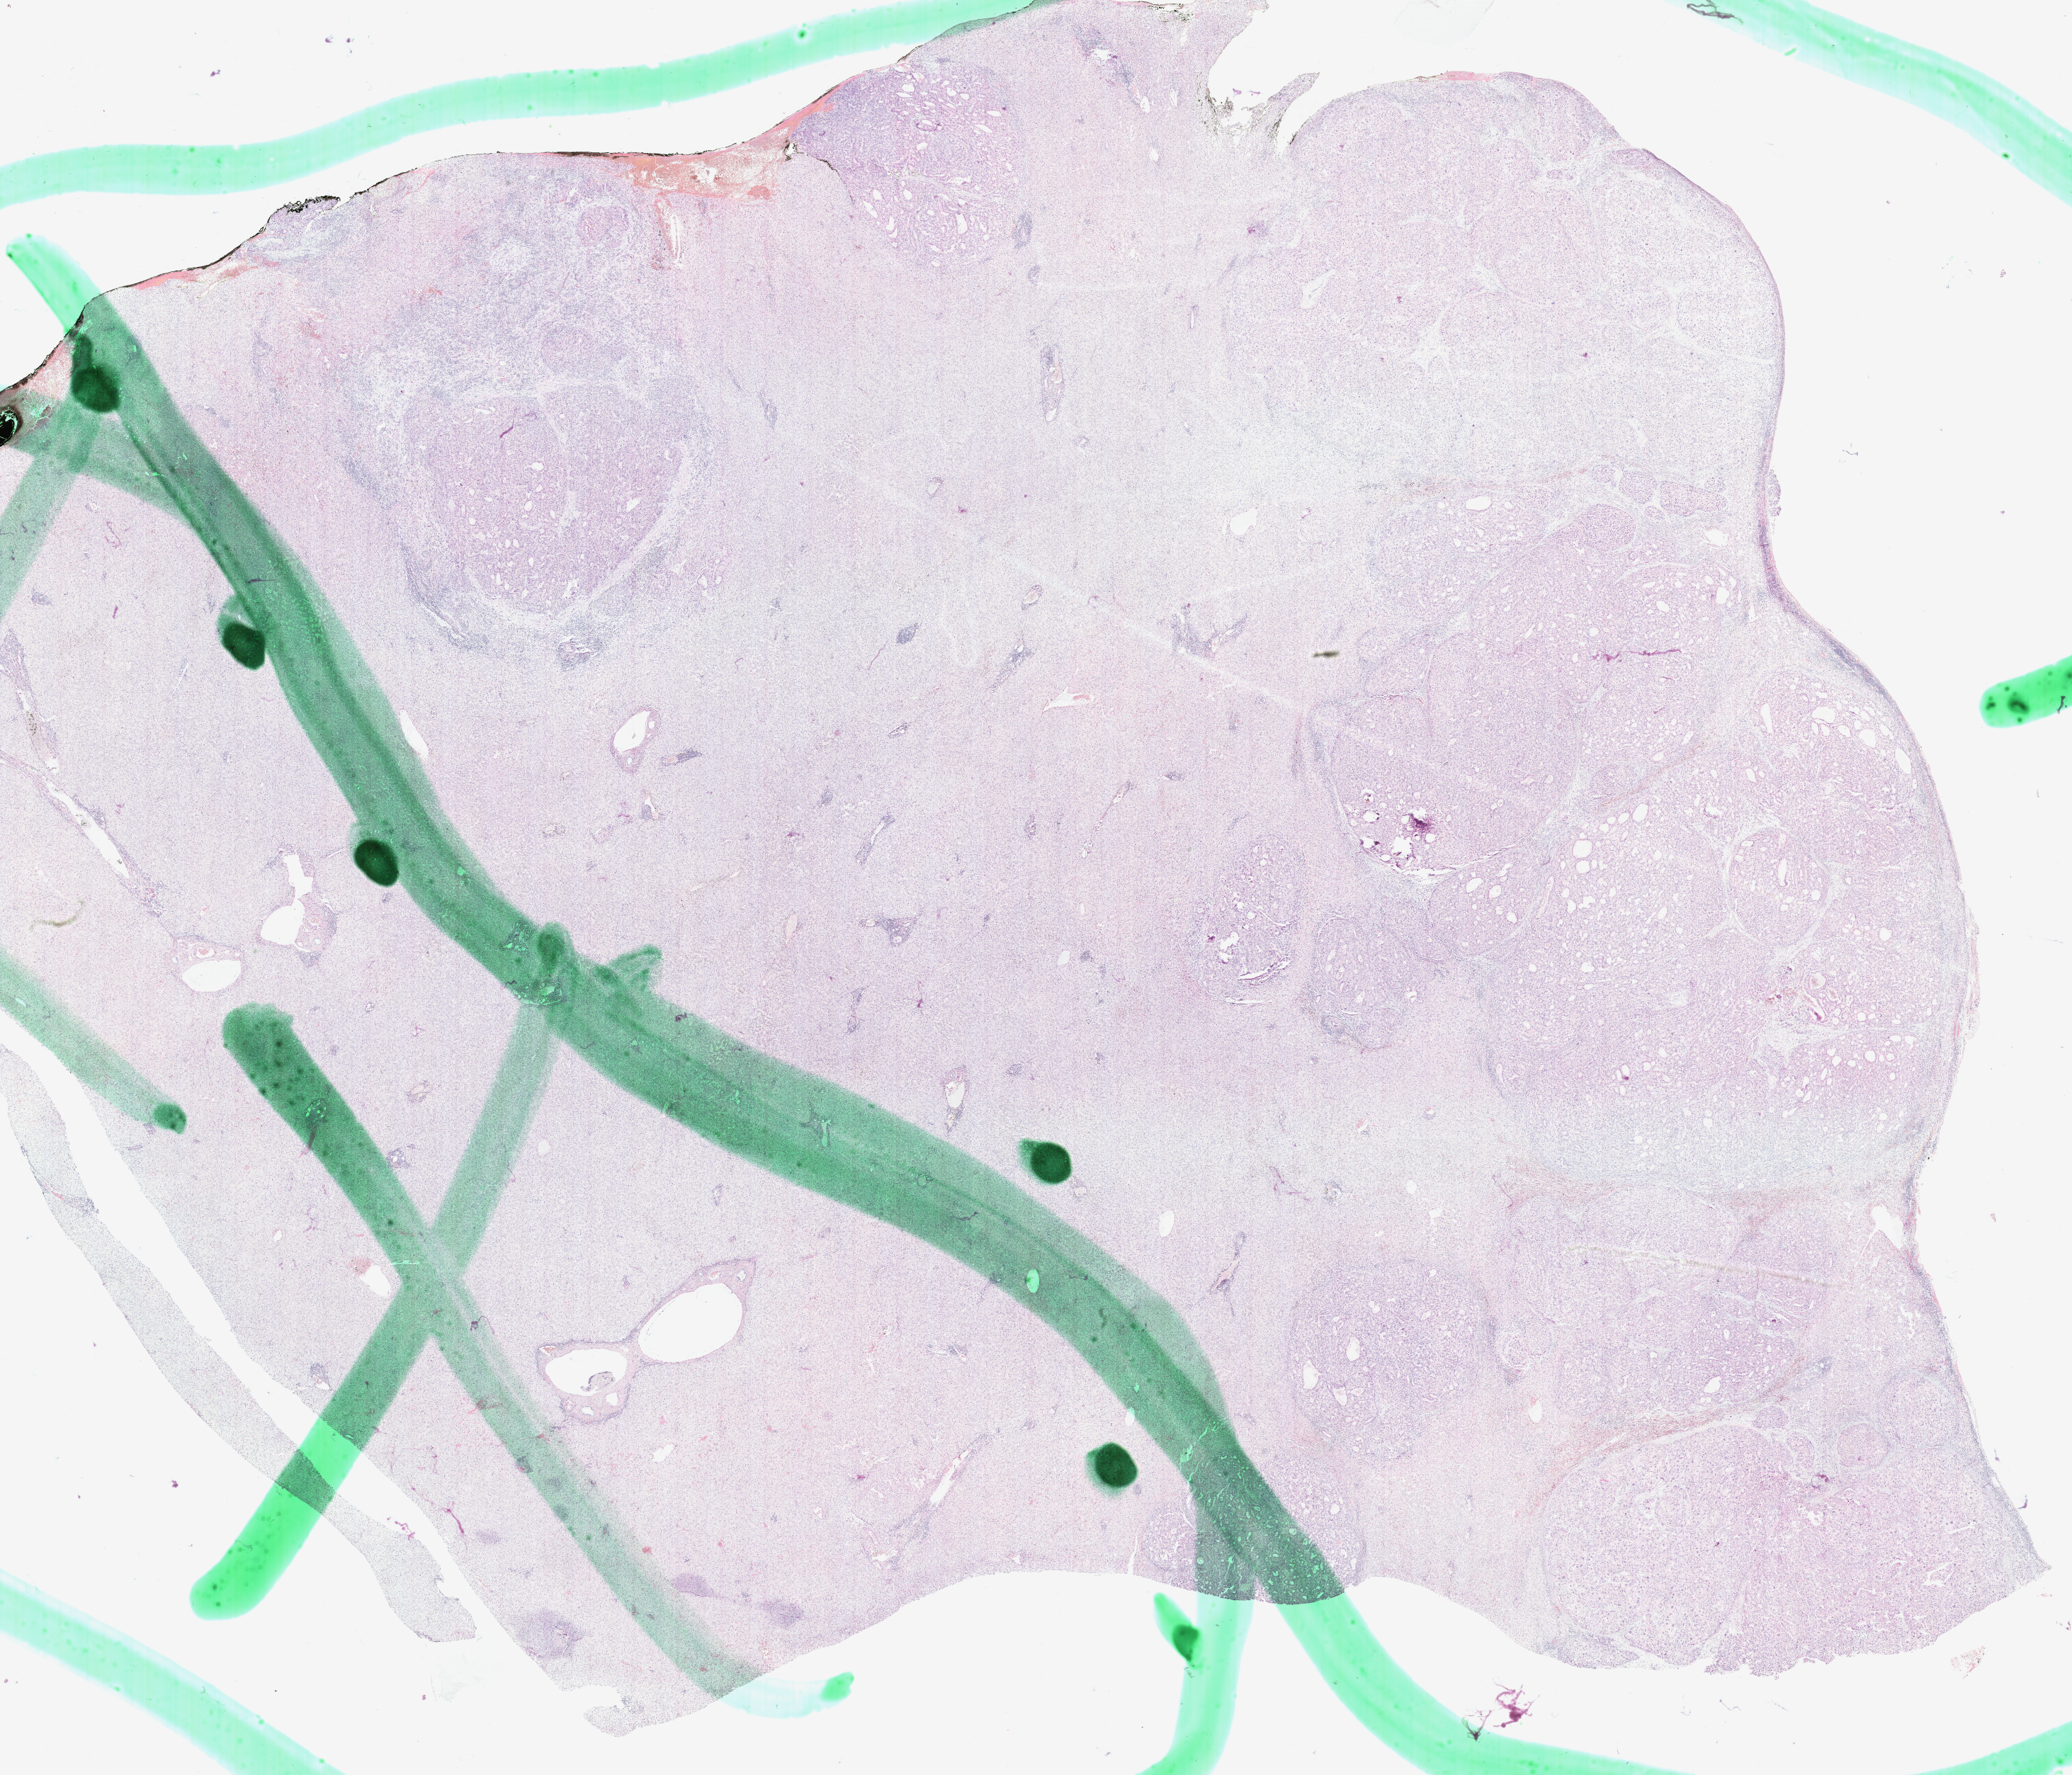
H&E whole-slide image, low-resolution overview of the scanned area, about 23.7 x 20.3 mm (slide scanned at 40x); FFPE section; liver, primary tumour sample. Female patient; age at initial diagnosis 74 years. Histologic grade: G2 (moderately differentiated).
* pathologic diagnosis: Hepatocellular carcinoma, NOS
* AJCC pathologic stage: IIIA (7th edition)